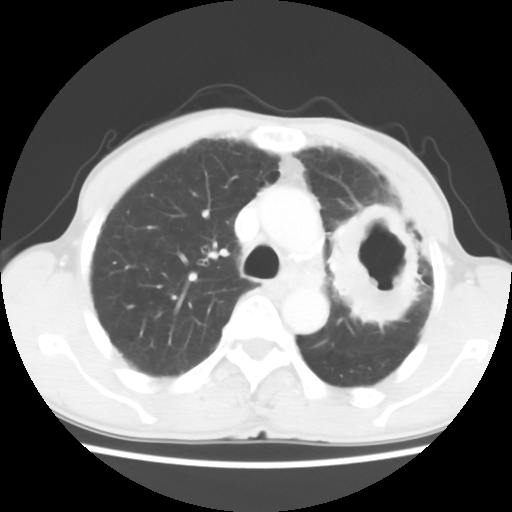
Chest CT, one axial slice. Slice 42 of 60 in the series (ordered by position). Reconstruction kernel STANDARD. Lung window (W 1500 / L -600 HU). 5 mm slice thickness. 512 × 512 image matrix, field of view 308 × 308 mm. Male patient, age 64 years. Case-level facts recorded for this patient, not image findings: clinical TNM (as recorded): T3 N3 M0.
Annotated regions visible in this slice (rectangle marked by the reading radiologist):
- lung tumour (recorded histology: adenocarcinoma): bounding box (x1, y1, x2, y2) in pixels: (321, 193, 424, 331)